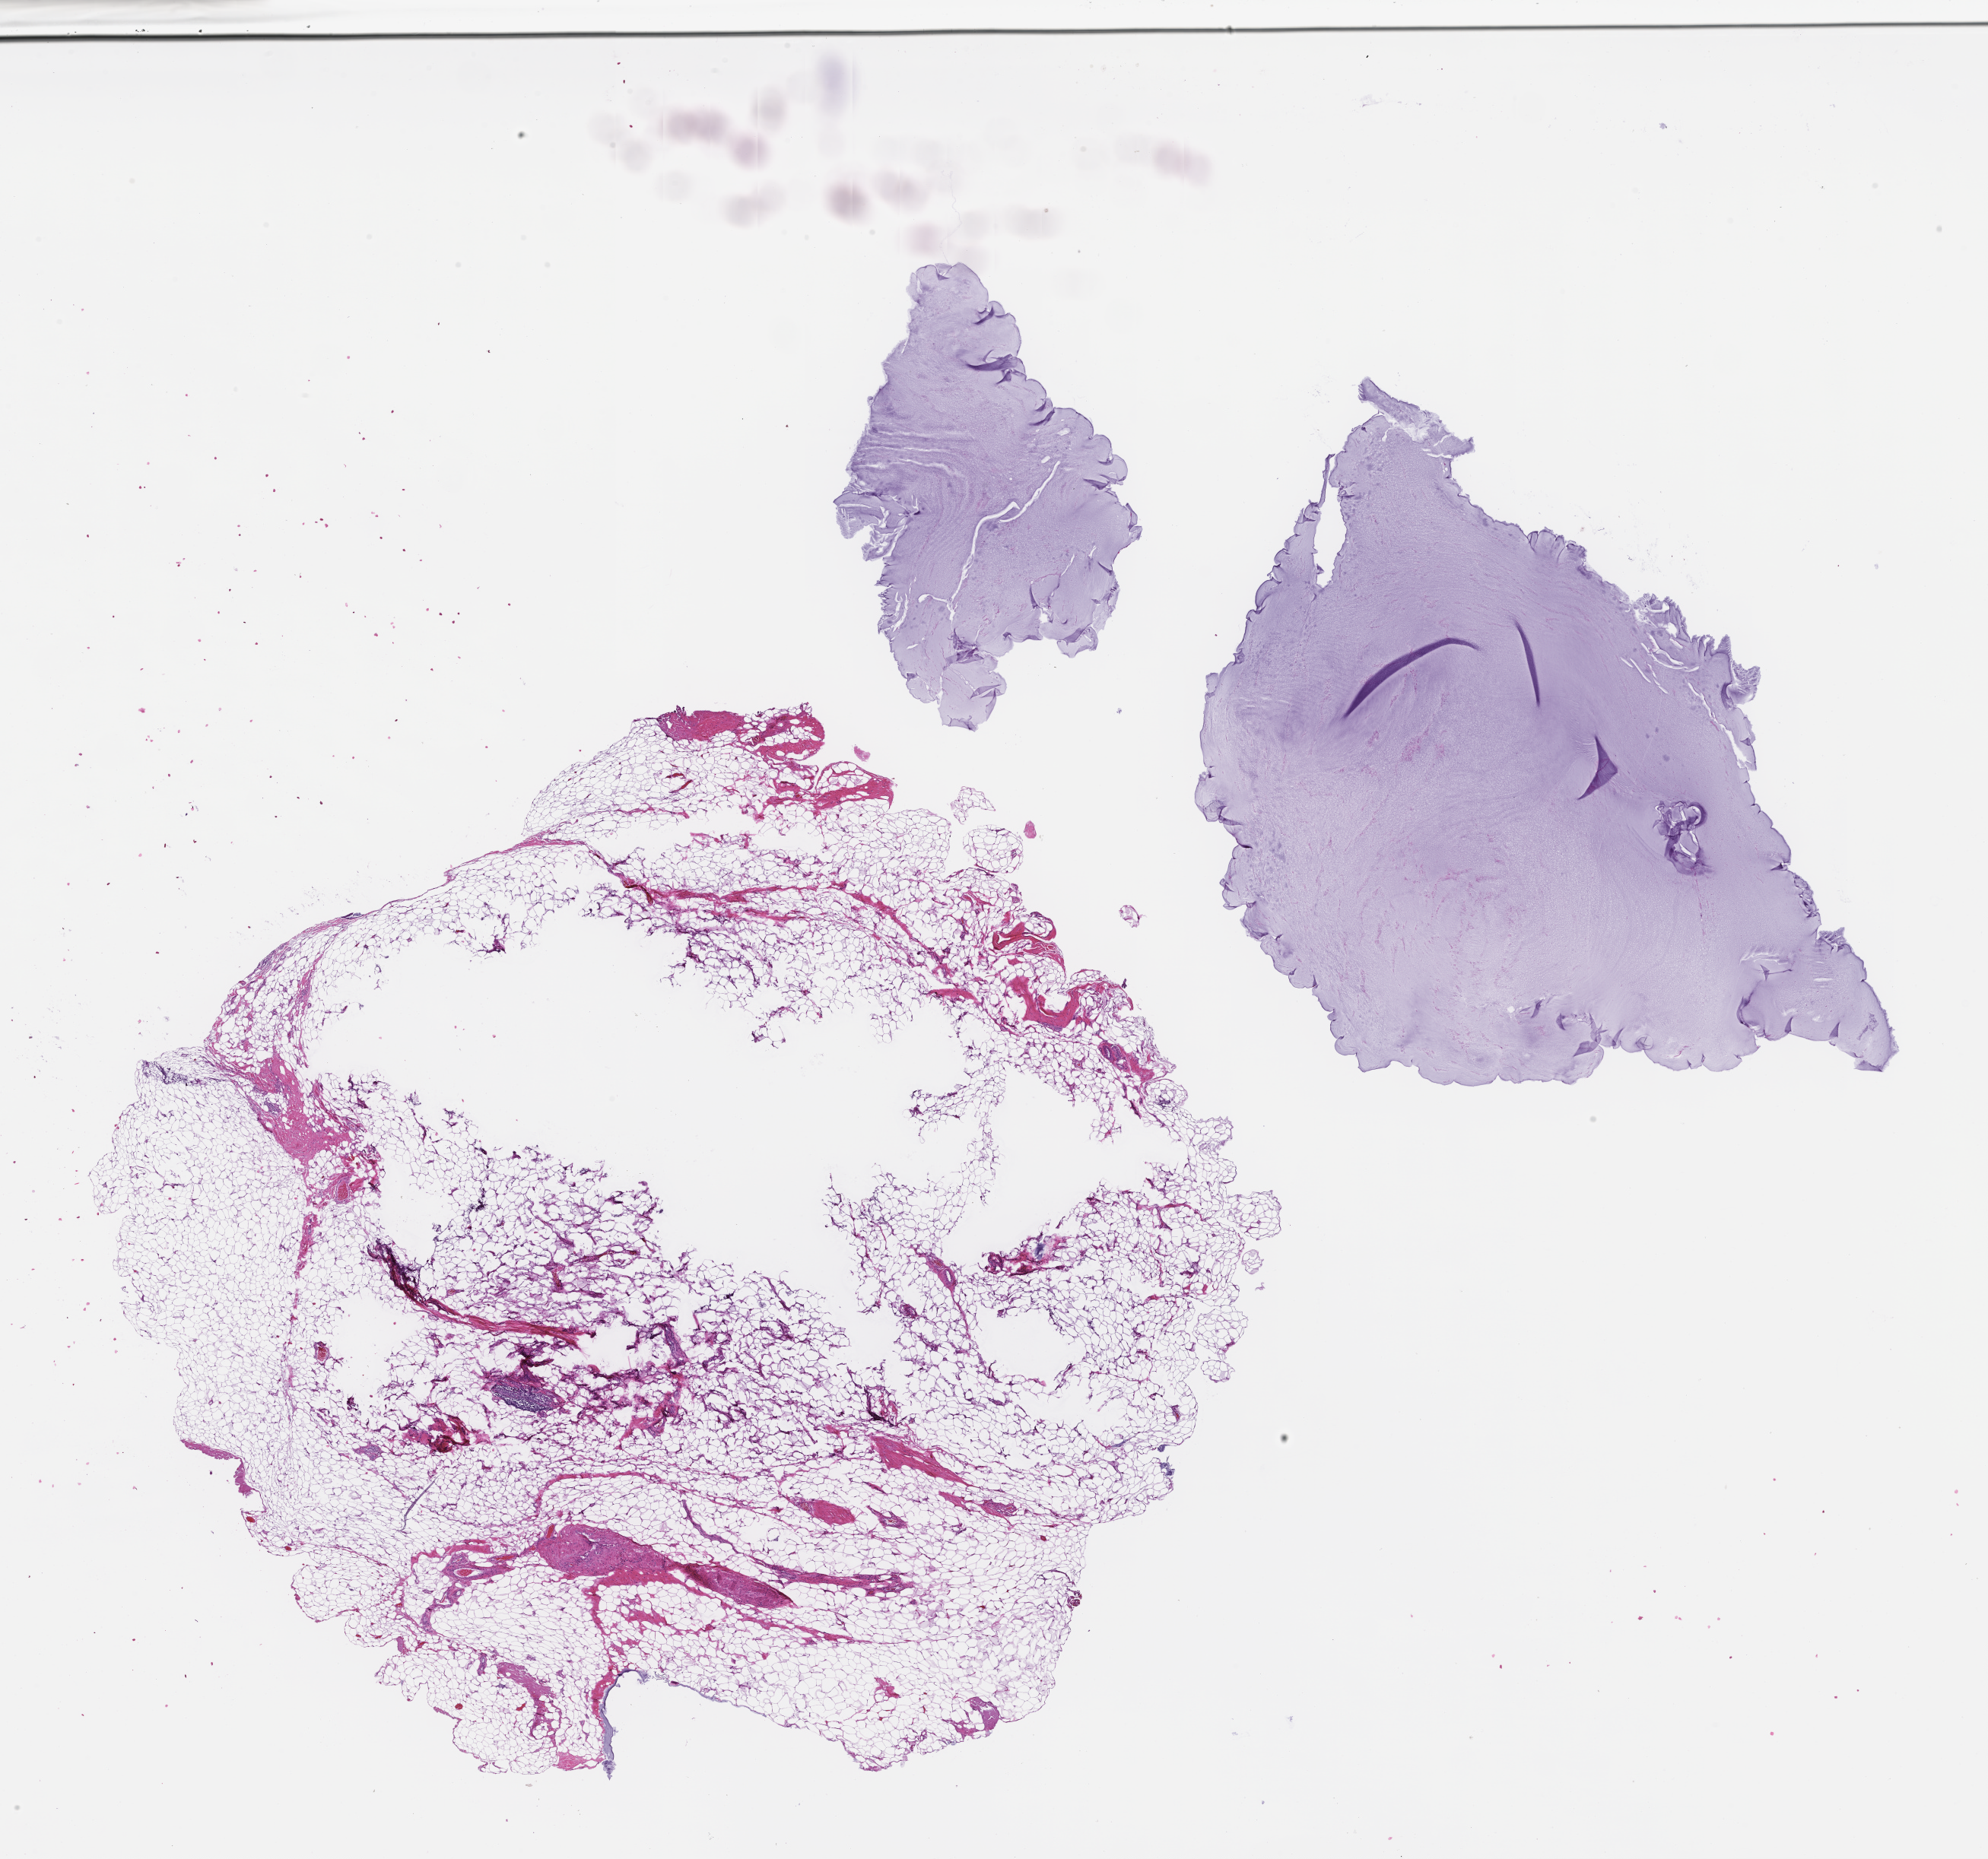
H&E whole-slide image — a low-resolution overview of the entire scanned area, about 21.1 x 19.7 mm, formalin-fixed, paraffin-embedded (FFPE) tissue, specimen time point: collected at baseline (before treatment). Male patient.
This section: metastatic tumor tissue. Patient diagnosis (primary): Colorectal Carcinoma.